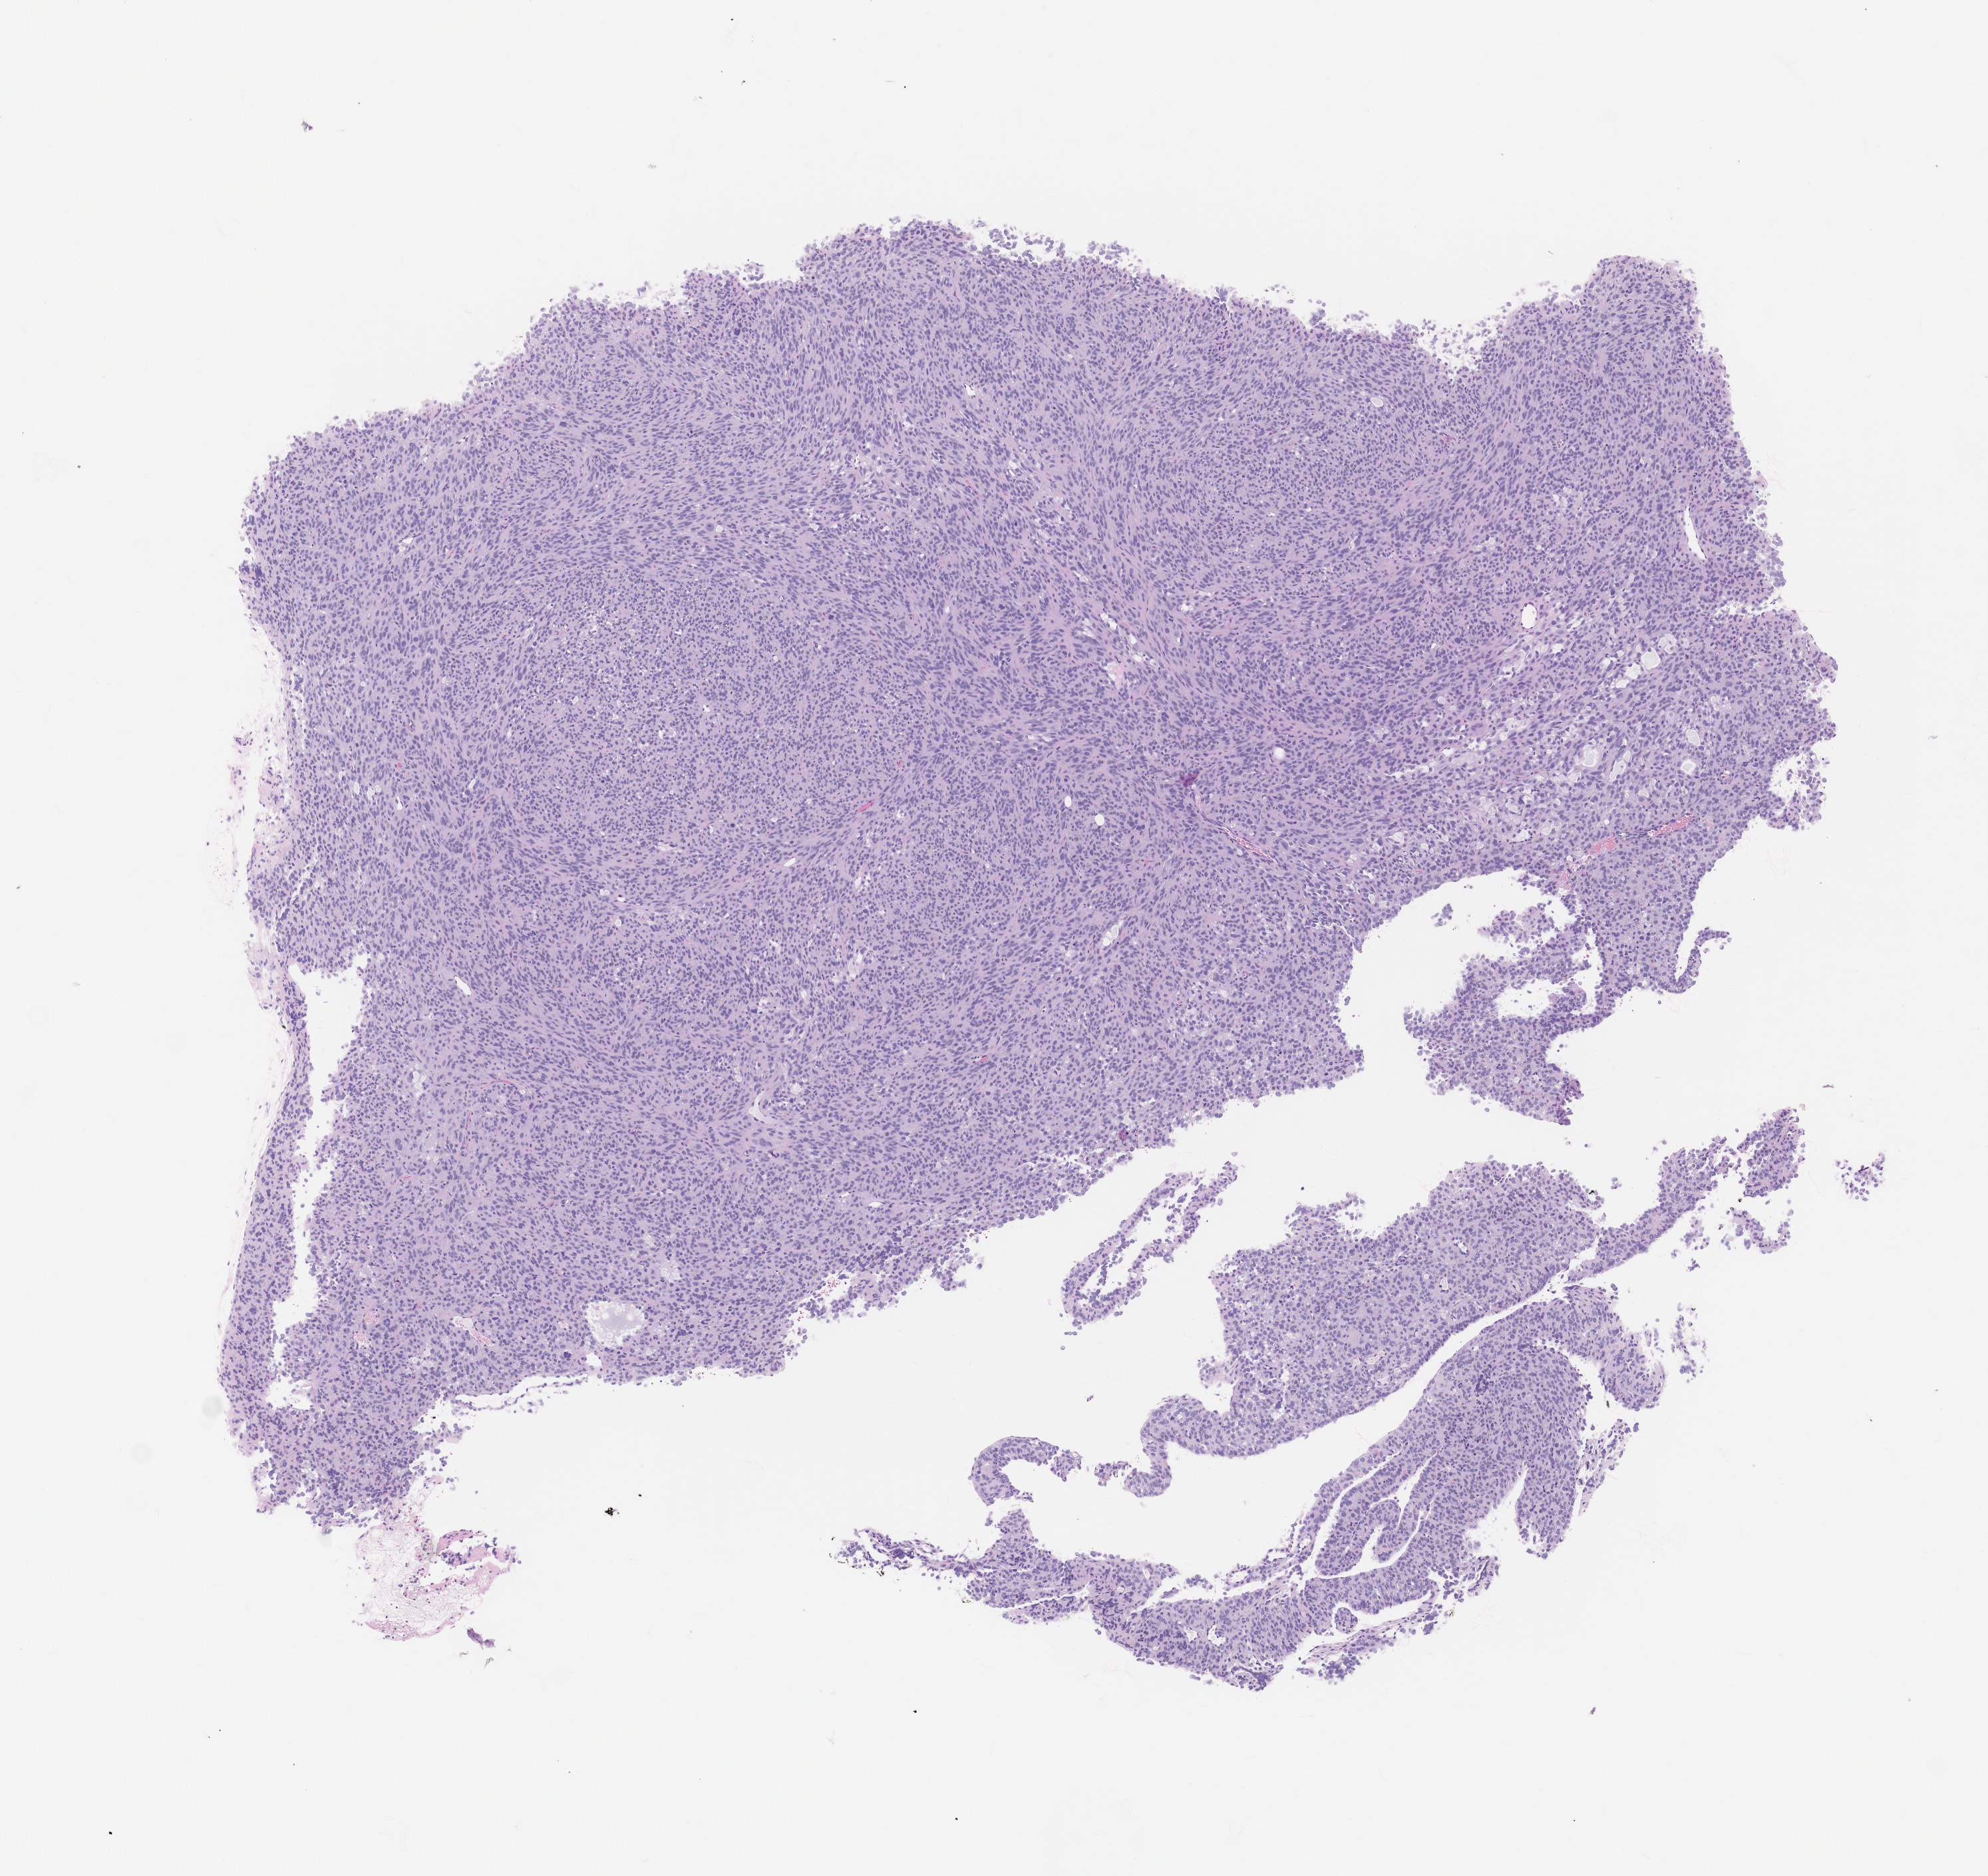
Whole-slide image, hematoxylin and eosin (H&E): patient-derived xenograft (human tumor grown in a mouse), passage 0, a low-resolution overview of the entire scanned area, about 6.0 x 5.7 mm; formalin-fixed, paraffin-embedded (FFPE) tissue; tumor site category: uterus.
- originating patient diagnosis: Leiomyosarcoma